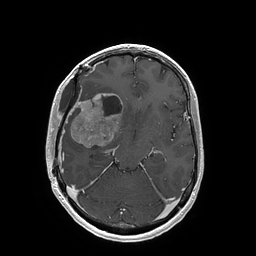
Brain MRI from a brain-tumour surgery series, one axial slice; slice 100 of 202 in the series (ordered by position); T1-weighted post-contrast; 1 mm slice thickness; 256 × 256 image matrix, field of view 250 × 250 mm. From the clinical record (not read from this slice): histopathology: Glioblastoma; WHO grade: 4; IDH mutation: no; tumour location: Right Insular.
Outlined on this slice (outlined manually by an expert reader):
- tumour: box from (x=70, y=93) to (x=122, y=148) px